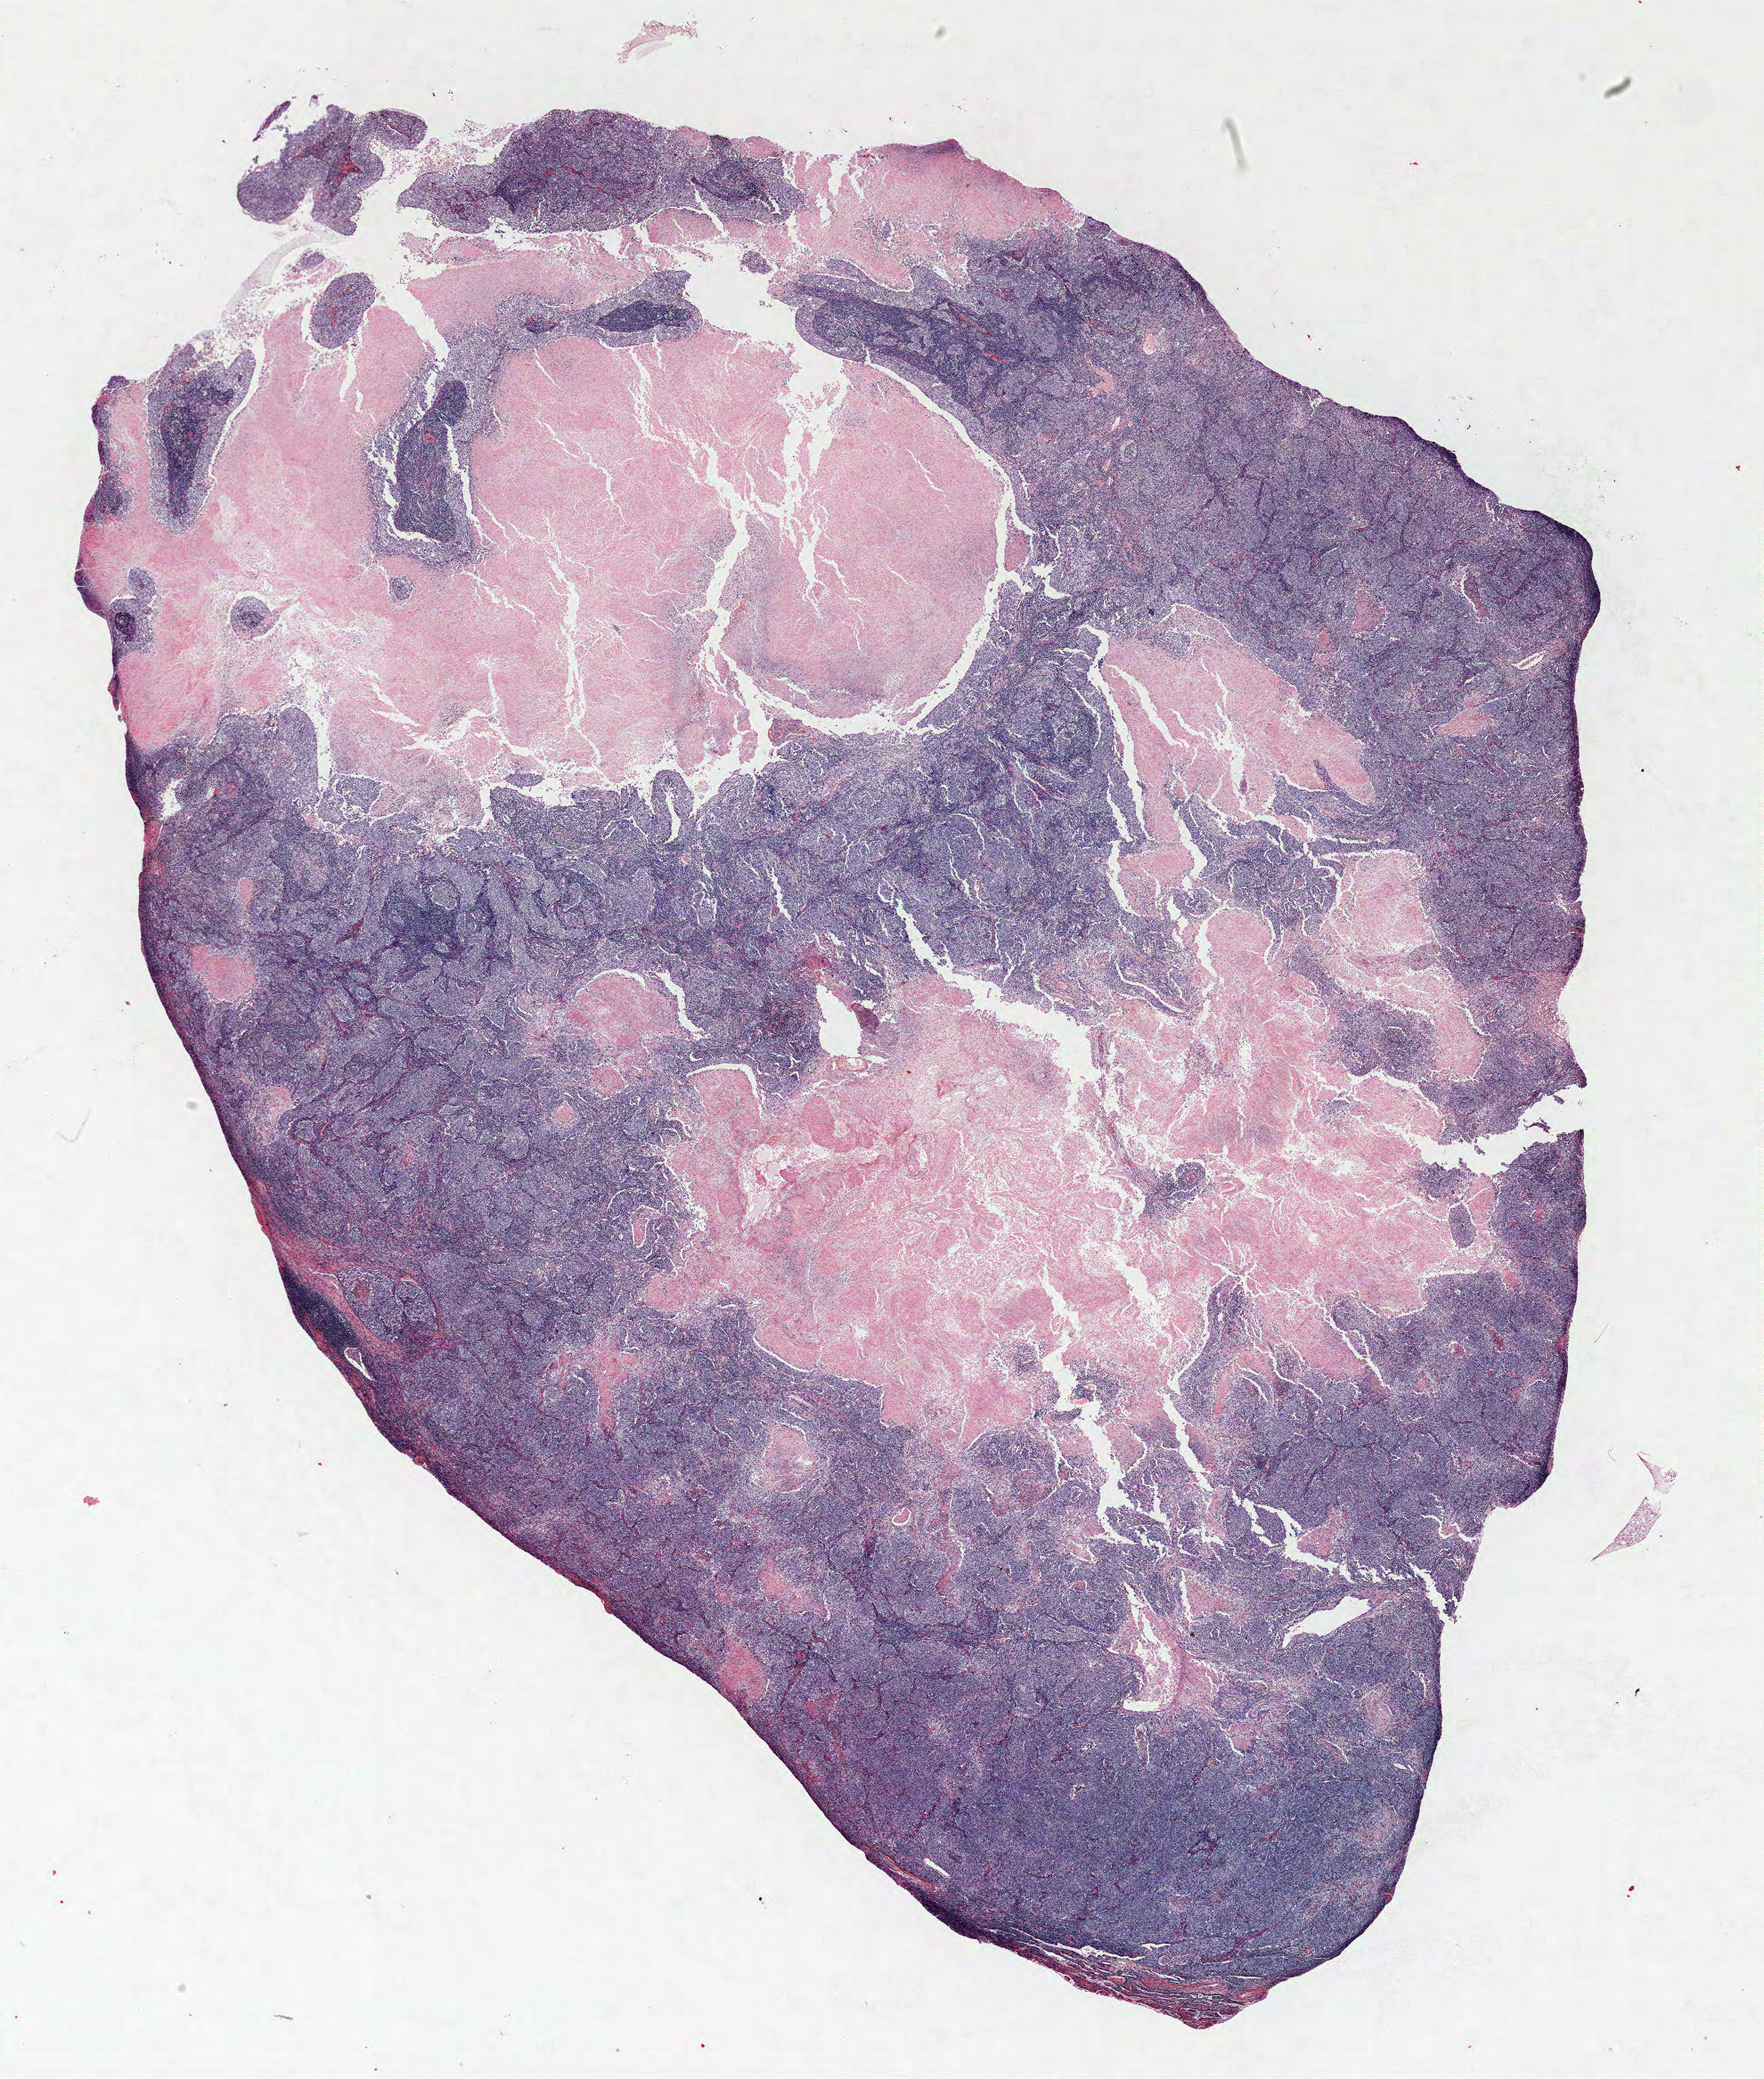
Hematoxylin and eosin (H&E) stained whole-slide image — low-resolution overview of the scanned area, about 15.8 x 18.7 mm (from a 40x scan), FFPE section, lung. Female, age 68 at enrolment. Former smoker at enrolment. Grade: poorly differentiated (G3).
* participant's lung-cancer diagnosis: Large cell carcinoma, NOS
* primary tumour location (clinical record): right lower lobe
* tumour size (pathology): 32 mm
* stage (AJCC 6th edition): IB
* ICD-O-3 topography: lower lobe of lung (C34.3)